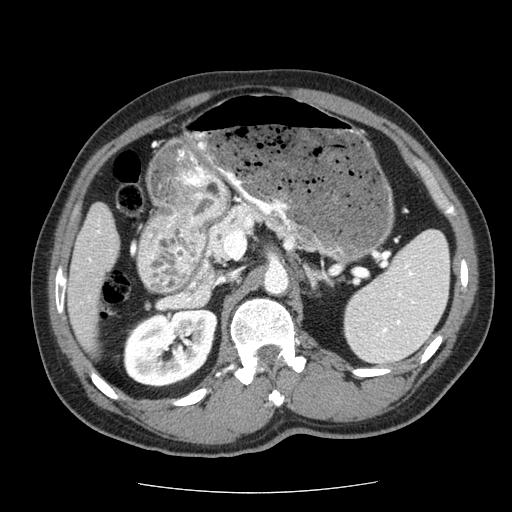
Contrast-enhanced abdominal CT (liver protocol), one axial slice. Position 20 of 85 along the scan axis. Reconstruction kernel STANDARD. Soft-tissue window (W 400 / L 40 HU). 512 × 512 image matrix, field of view 360 × 360 mm. Case-level facts recorded for this patient, not image findings: diagnosis: hepatocellular carcinoma (patient treated with transarterial chemoembolisation; whether this scan precedes or follows treatment is not stated here); TNM stage (as recorded): Stage-IIIA; Child-Pugh class: A; tumour differentiation: well differentiated; tumour nodularity: multinodular.
Structures marked on this image (semi-automatically segmented with operator editing):
- liver parenchyma outside the tumour (the mass and vessels are separate outlines, so this box may not span the whole liver): bounding box <68,202,118,355> (left, top, right, bottom; pixels)
- liver vessels: <89,230,101,261>